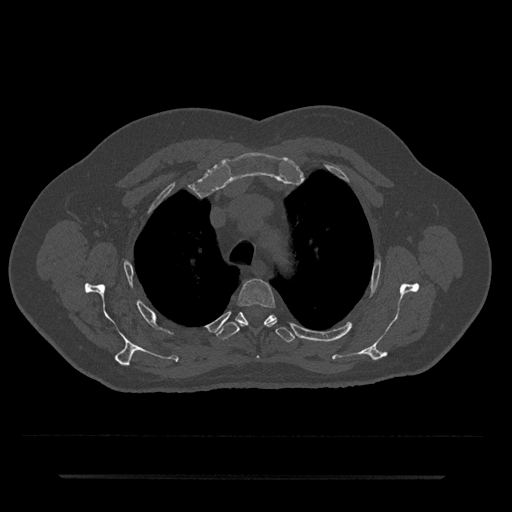
CT including the spine, one axial slice; reconstruction kernel Br40s/3; 120 kVp; bone window (W 1800 / L 400 HU); 512 × 512 image matrix, field of view 437 × 437 mm. Male patient, age 69 years. From the clinical record (not read from this slice): primary cancer: prostate.
Outlined on this slice (semi-automatically segmented with operator editing):
- T3 vertebra: bounding box (x1, y1, x2, y2) in pixels: (237, 279, 276, 358)
- T4 vertebra: (216, 312, 295, 342)